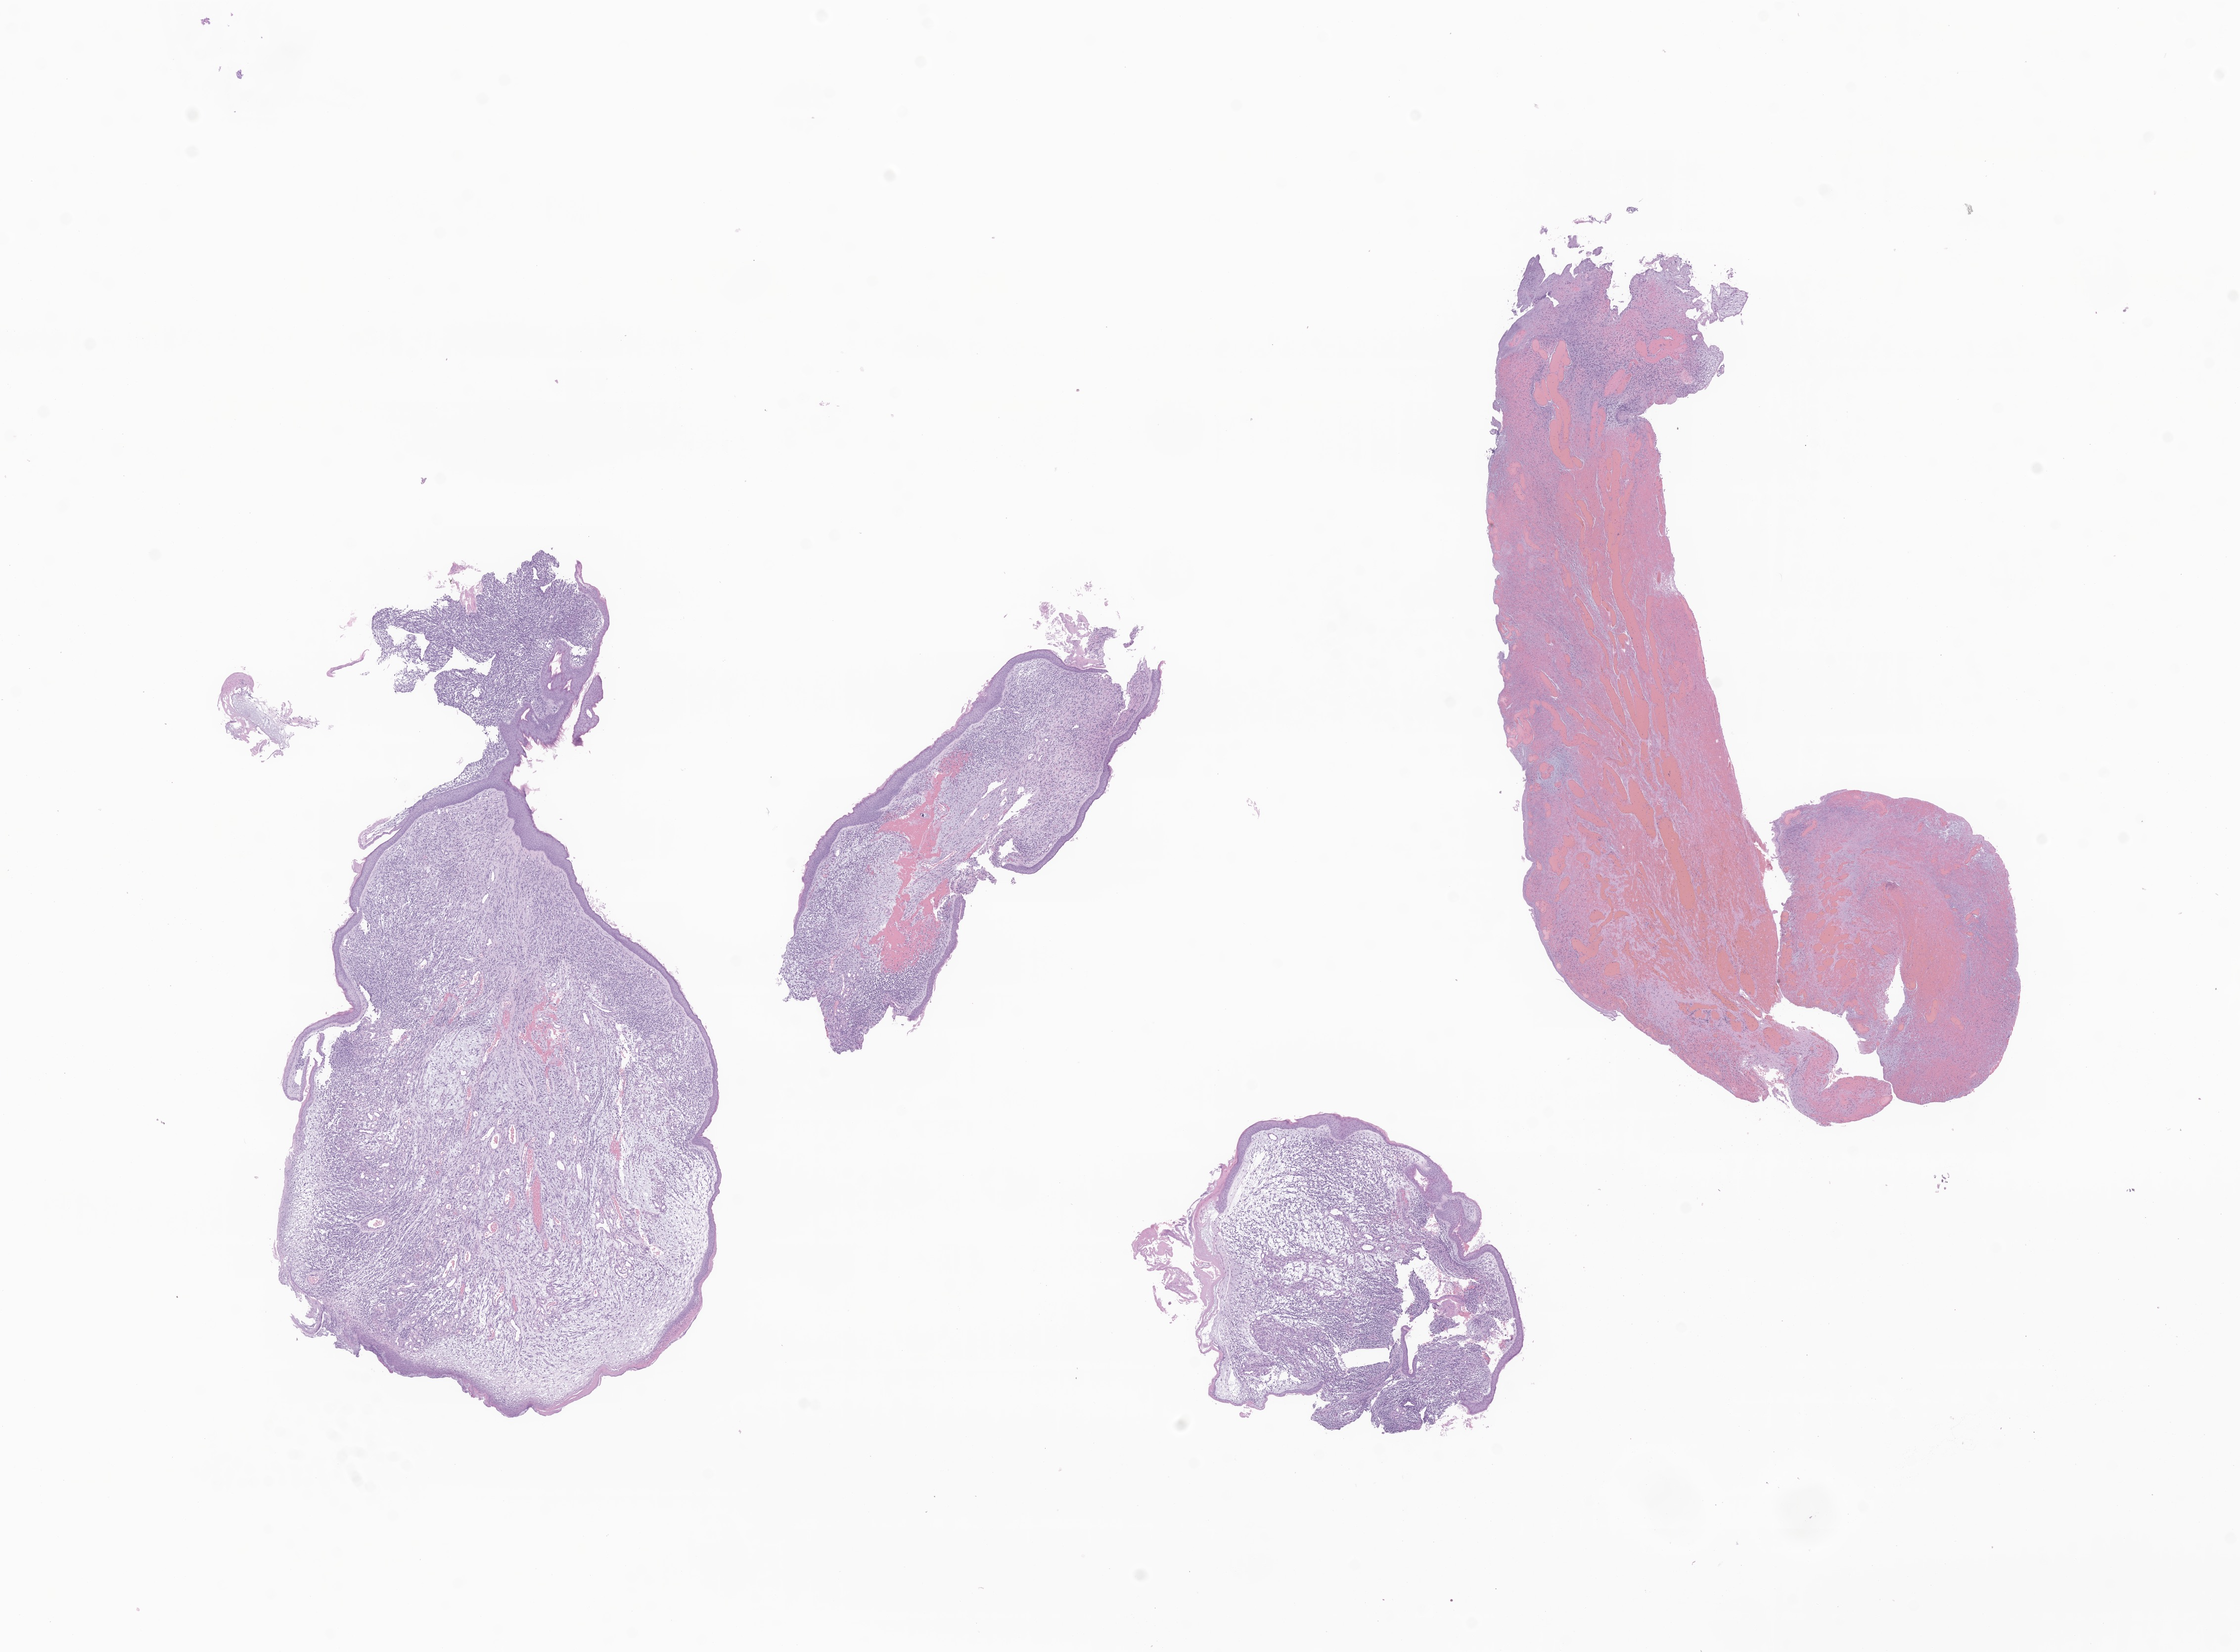
Digitized haematoxylin and eosin-stained section of tumor tissue from the external ear — low-resolution overview of the scanned area, about 19.1 x 14.1 mm. FFPE section. Male patient, age 365 days (about 1.0 years).
Diagnosis (ICD-O-3 morphology term): Embryonal rhabdomyosarcoma, NOS.